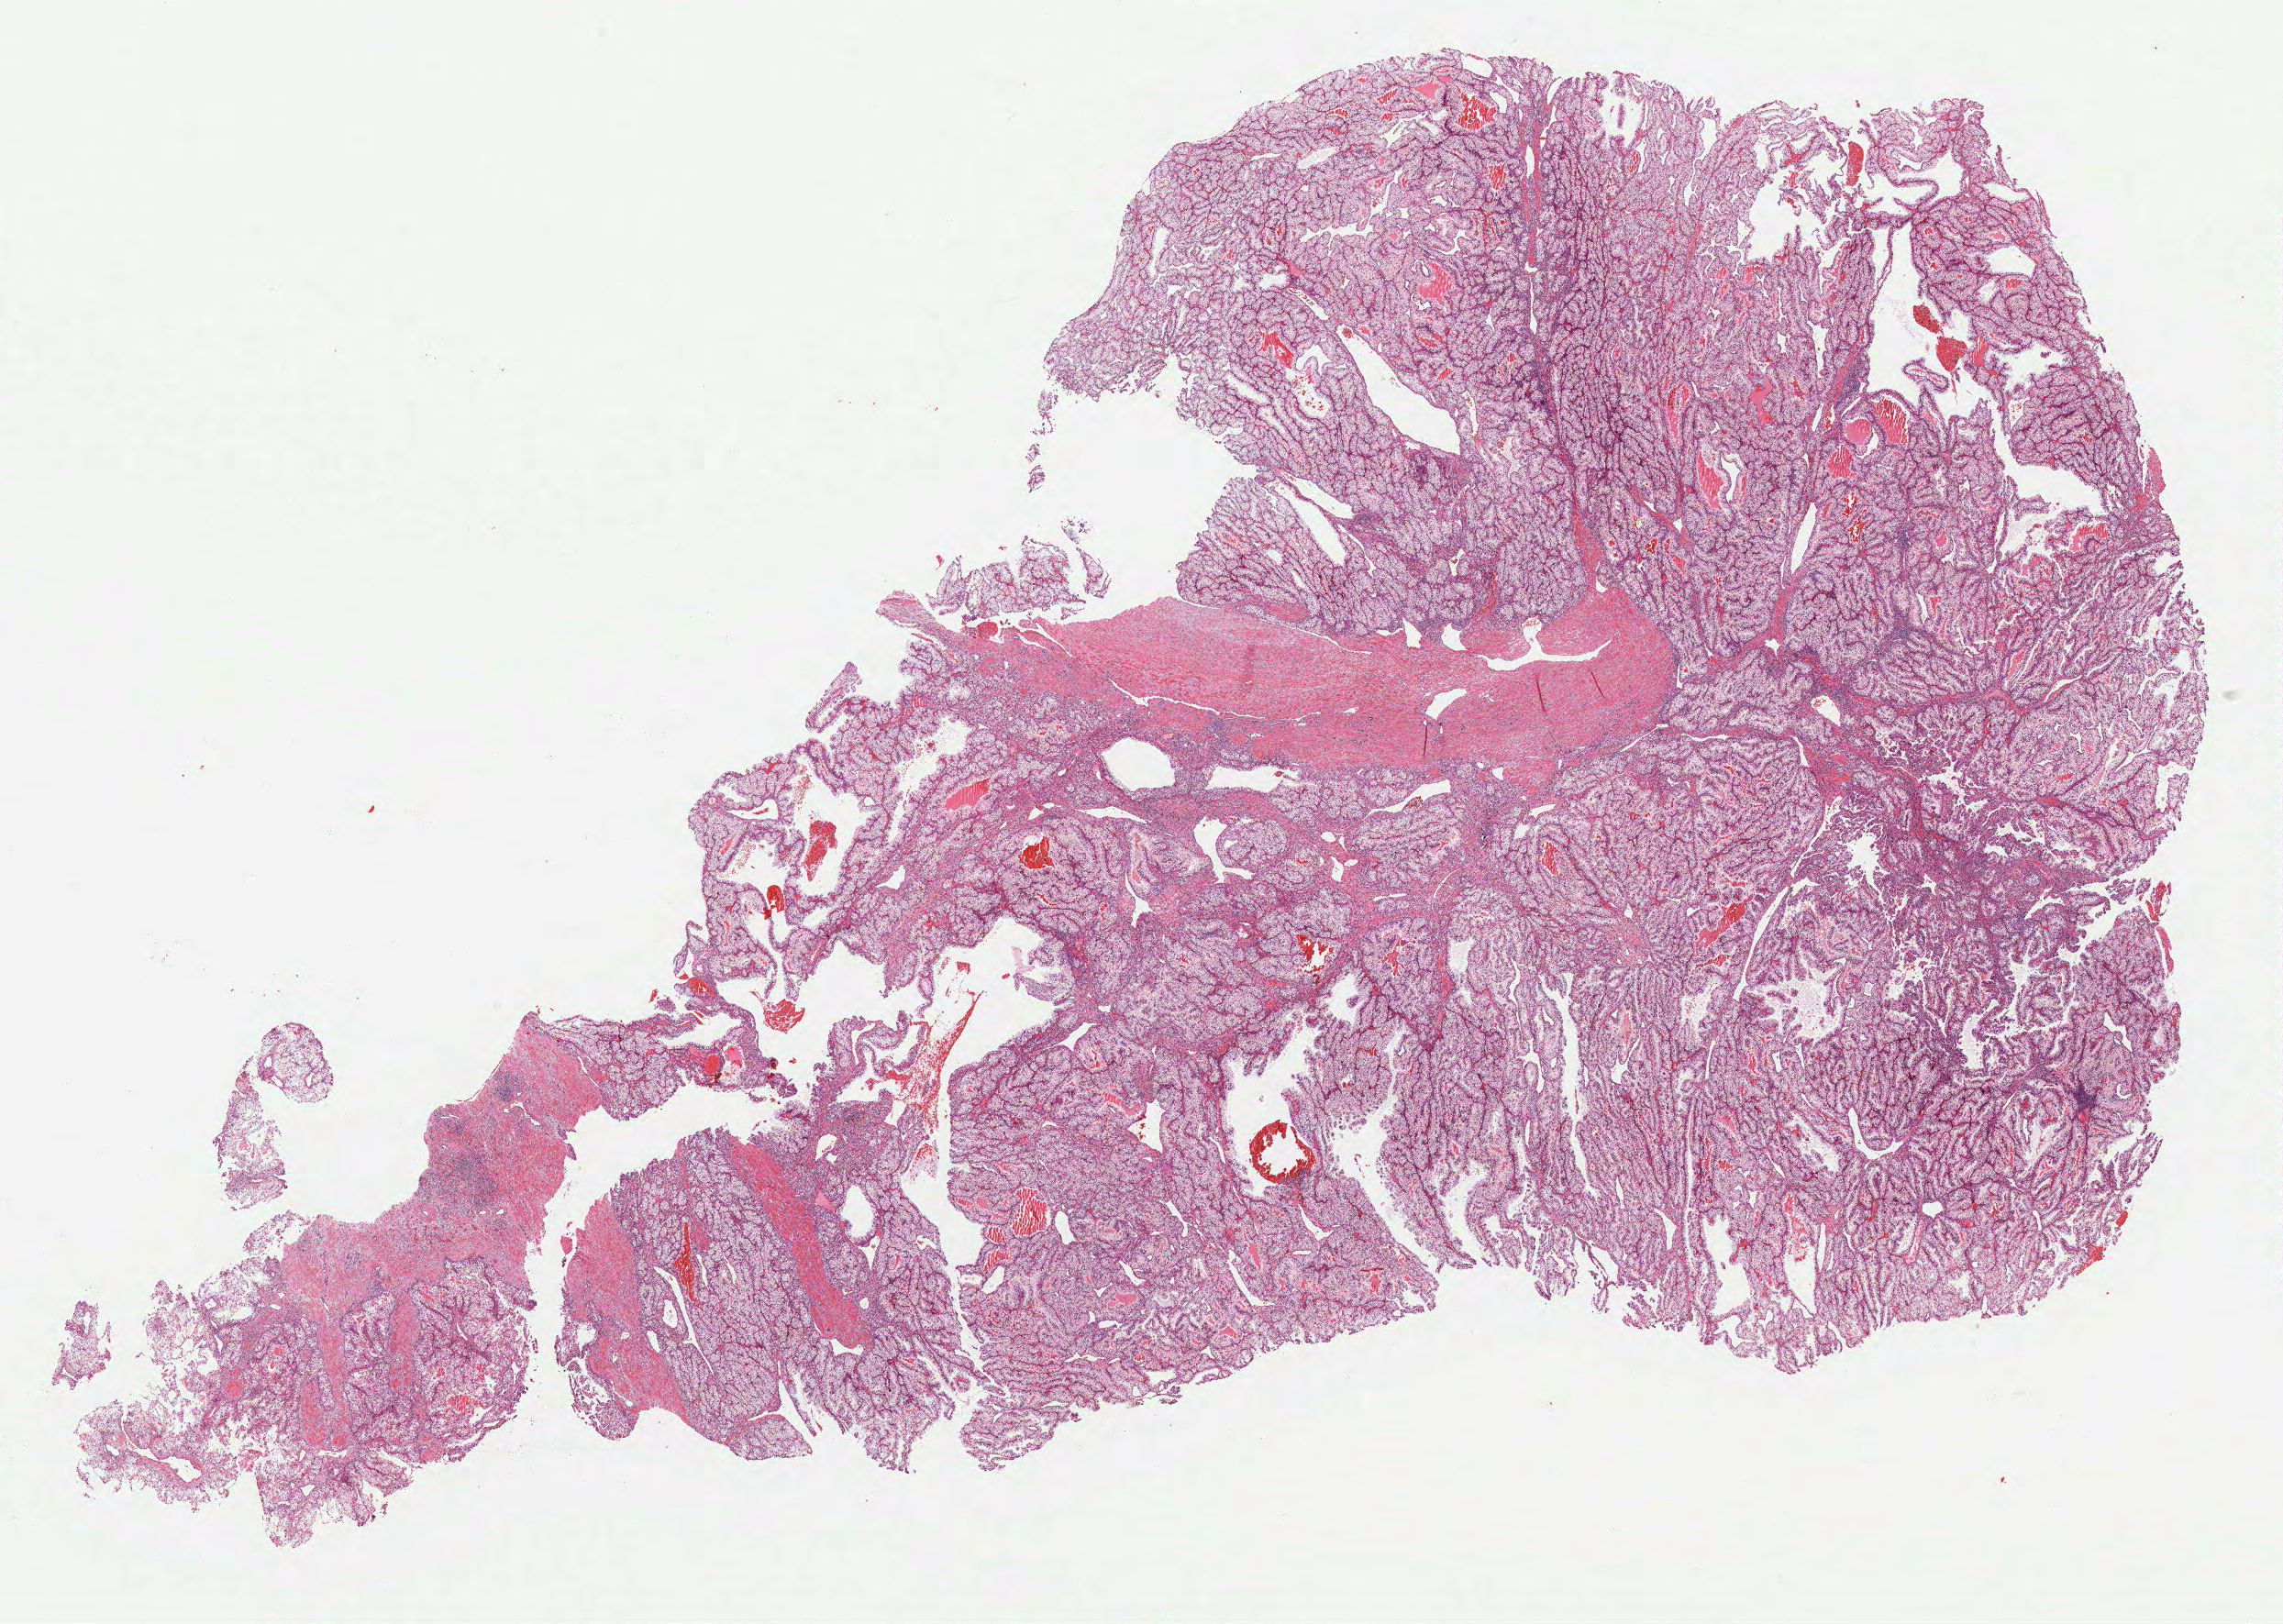
Whole-slide histology image, Hematoxylin and eosin (H&E) stained, a low-resolution overview of the entire scanned area, about 20.1 x 14.3 mm (acquisition: 40x scan), formalin-fixed paraffin-embedded (FFPE) diagnostic section, primary tumour sample from the kidney. Male patient; age at initial diagnosis 38 years. Histologic grade: G2 (moderately differentiated).
AJCC pathologic stage: I. Histologic diagnosis: Clear cell adenocarcinoma, NOS.